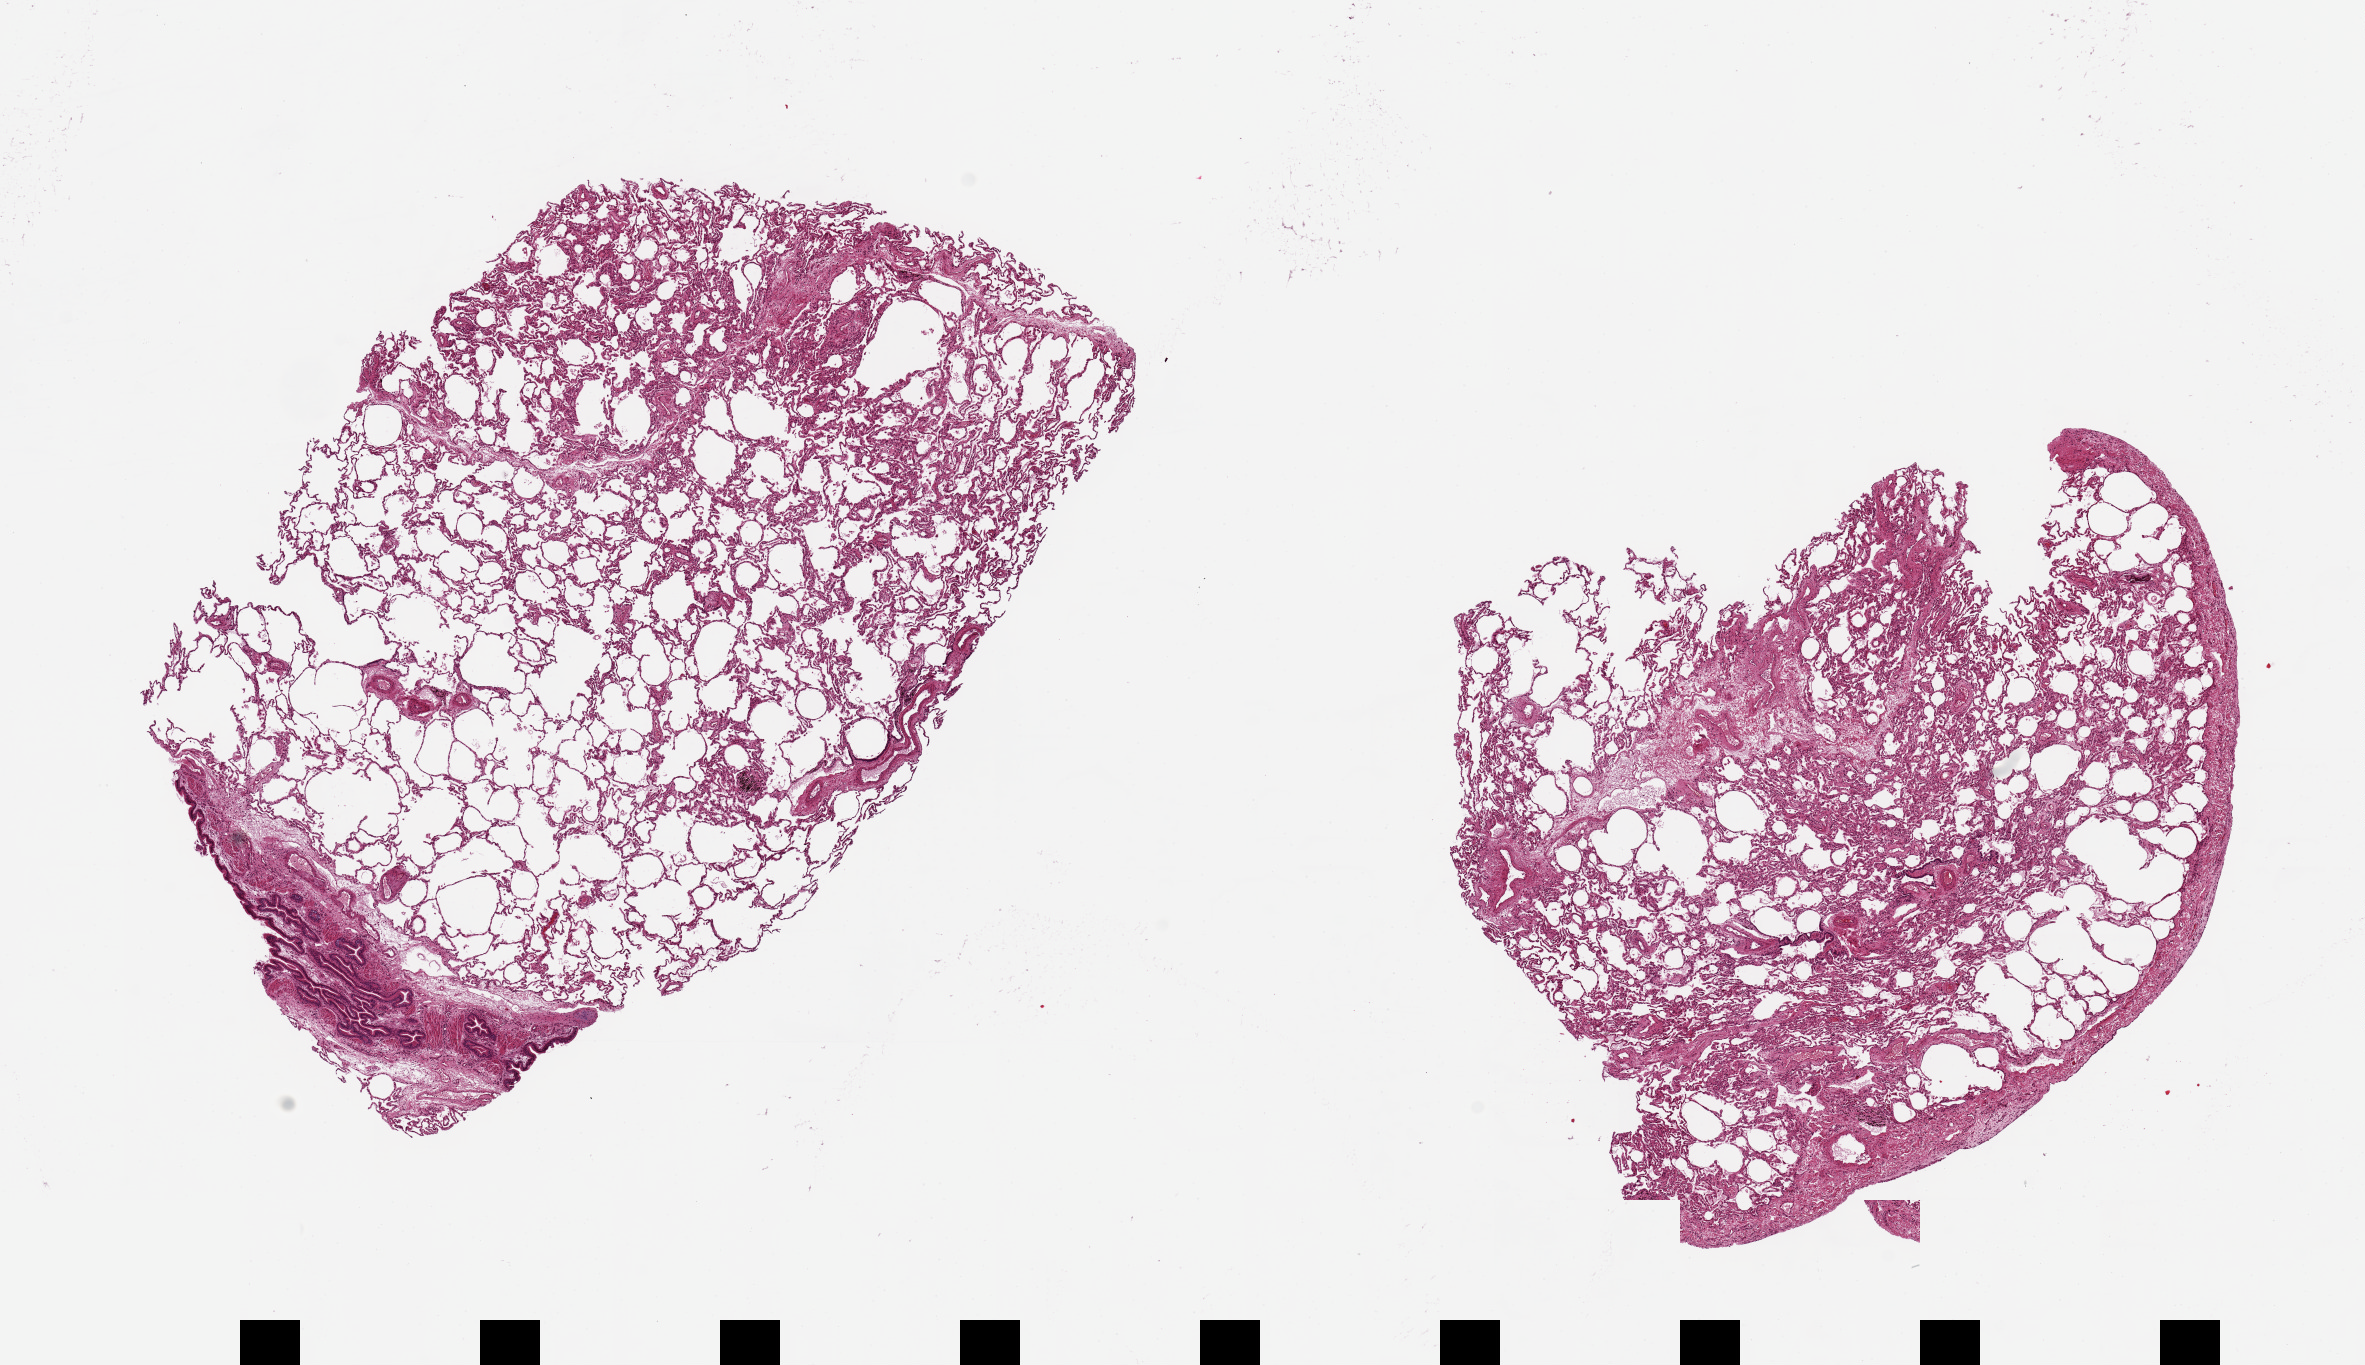
Whole-slide image, hematoxylin and eosin (H&E) stain, brightfield, whole scanned area (about 18.7 x 10.8 mm, slide scanned at 20x) shown as a low-resolution overview; PAXgene-fixed, paraffin-embedded tissue; section of lung (target tissue); donor tissue sample. Donor: male.
• review note (as recorded): 2 pieces, 8.5x5.5 & 7x6mm; 1 piece has pleura (tissue should be sampled >1 cm beneath pleura)